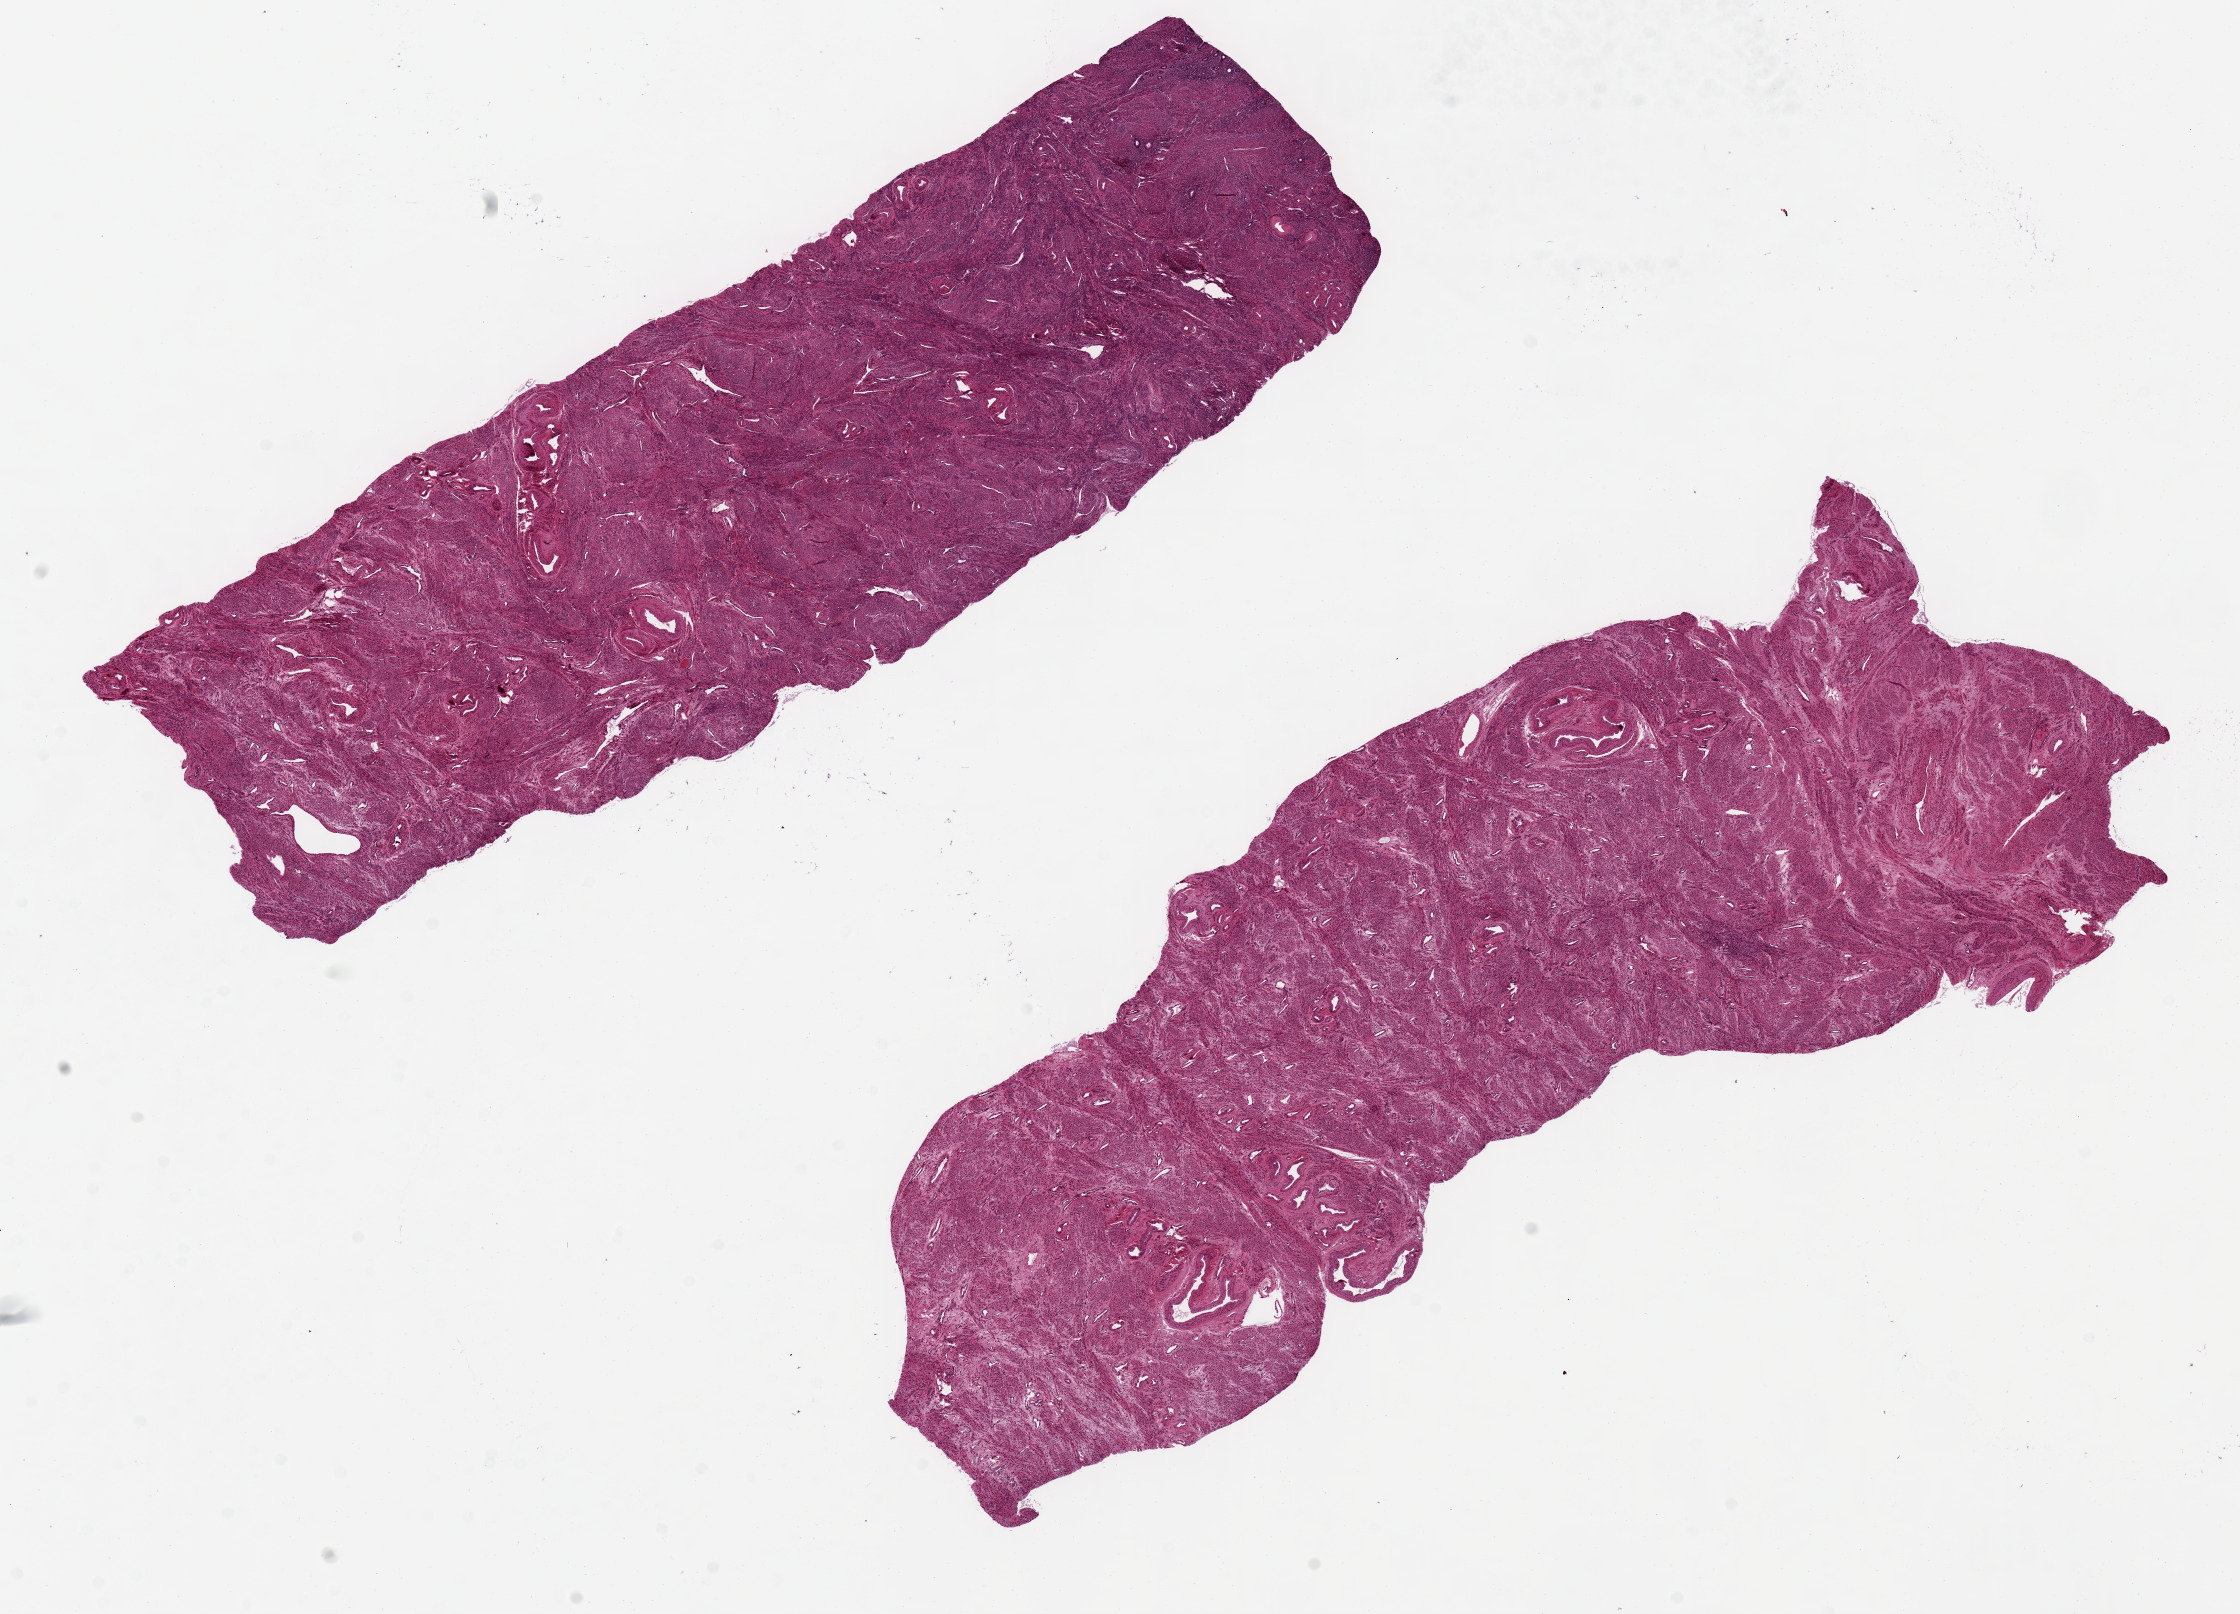
Digitized hematoxylin and eosin (H&E)-stained section — low-resolution overview of the scanned area, about 17.7 x 12.8 mm. PAXgene-fixed, paraffin-embedded tissue. Section of uterus (target tissue). Tissue donor sample. Female donor.
• review note (as recorded): 2 aliquots ~10x3mm. Trace minute glands, adenomyosis